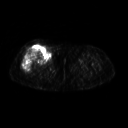
FDG PET of an extremity soft-tissue mass (from a PET/CT study), one axial slice; slice 251 of 311 in the series (ordered by position); 3.27 mm slice thickness; 128 × 128 image matrix, field of view 500 × 500 mm. Female patient, age 57 years. From the clinical record (not read from this slice): histological type: pleiomorphic undifferentiated sarcoma; grade: high; site of the primary tumour: right quadricep.
Outlined on this slice (expert contour drawn on MRI and transferred to this co-registered scan by the dataset authors):
- tumour plus oedema (research contour): bounding box <23,45,50,72> (left, top, right, bottom; pixels)
- tumour (research contour): <23,45,50,72>